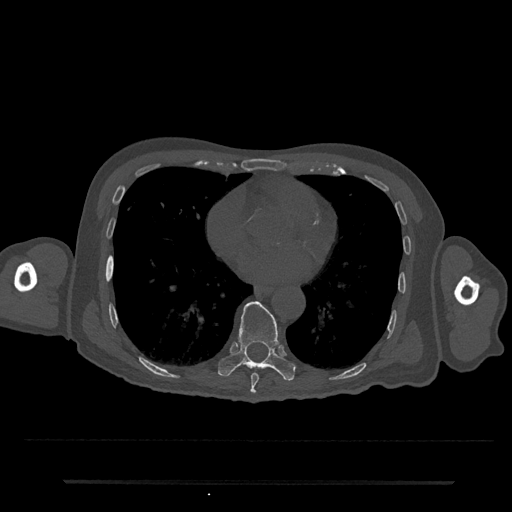
CT including the spine, one axial slice. Position 380 of 797 along the scan axis. Reconstruction kernel Br40s/3. 120 kVp. Bone window (W 1800 / L 400 HU). 0.5 mm slice thickness. 512 × 512 image matrix, field of view 427 × 427 mm. Male patient, age 74 years. Case-level facts recorded for this patient, not image findings: primary cancer: prostate.
Annotated regions visible in this slice (semi-automatically segmented with operator editing):
- T8 vertebra: box from (x=250, y=373) to (x=259, y=394) px
- T9 vertebra: (x=218, y=301)–(x=295, y=381)